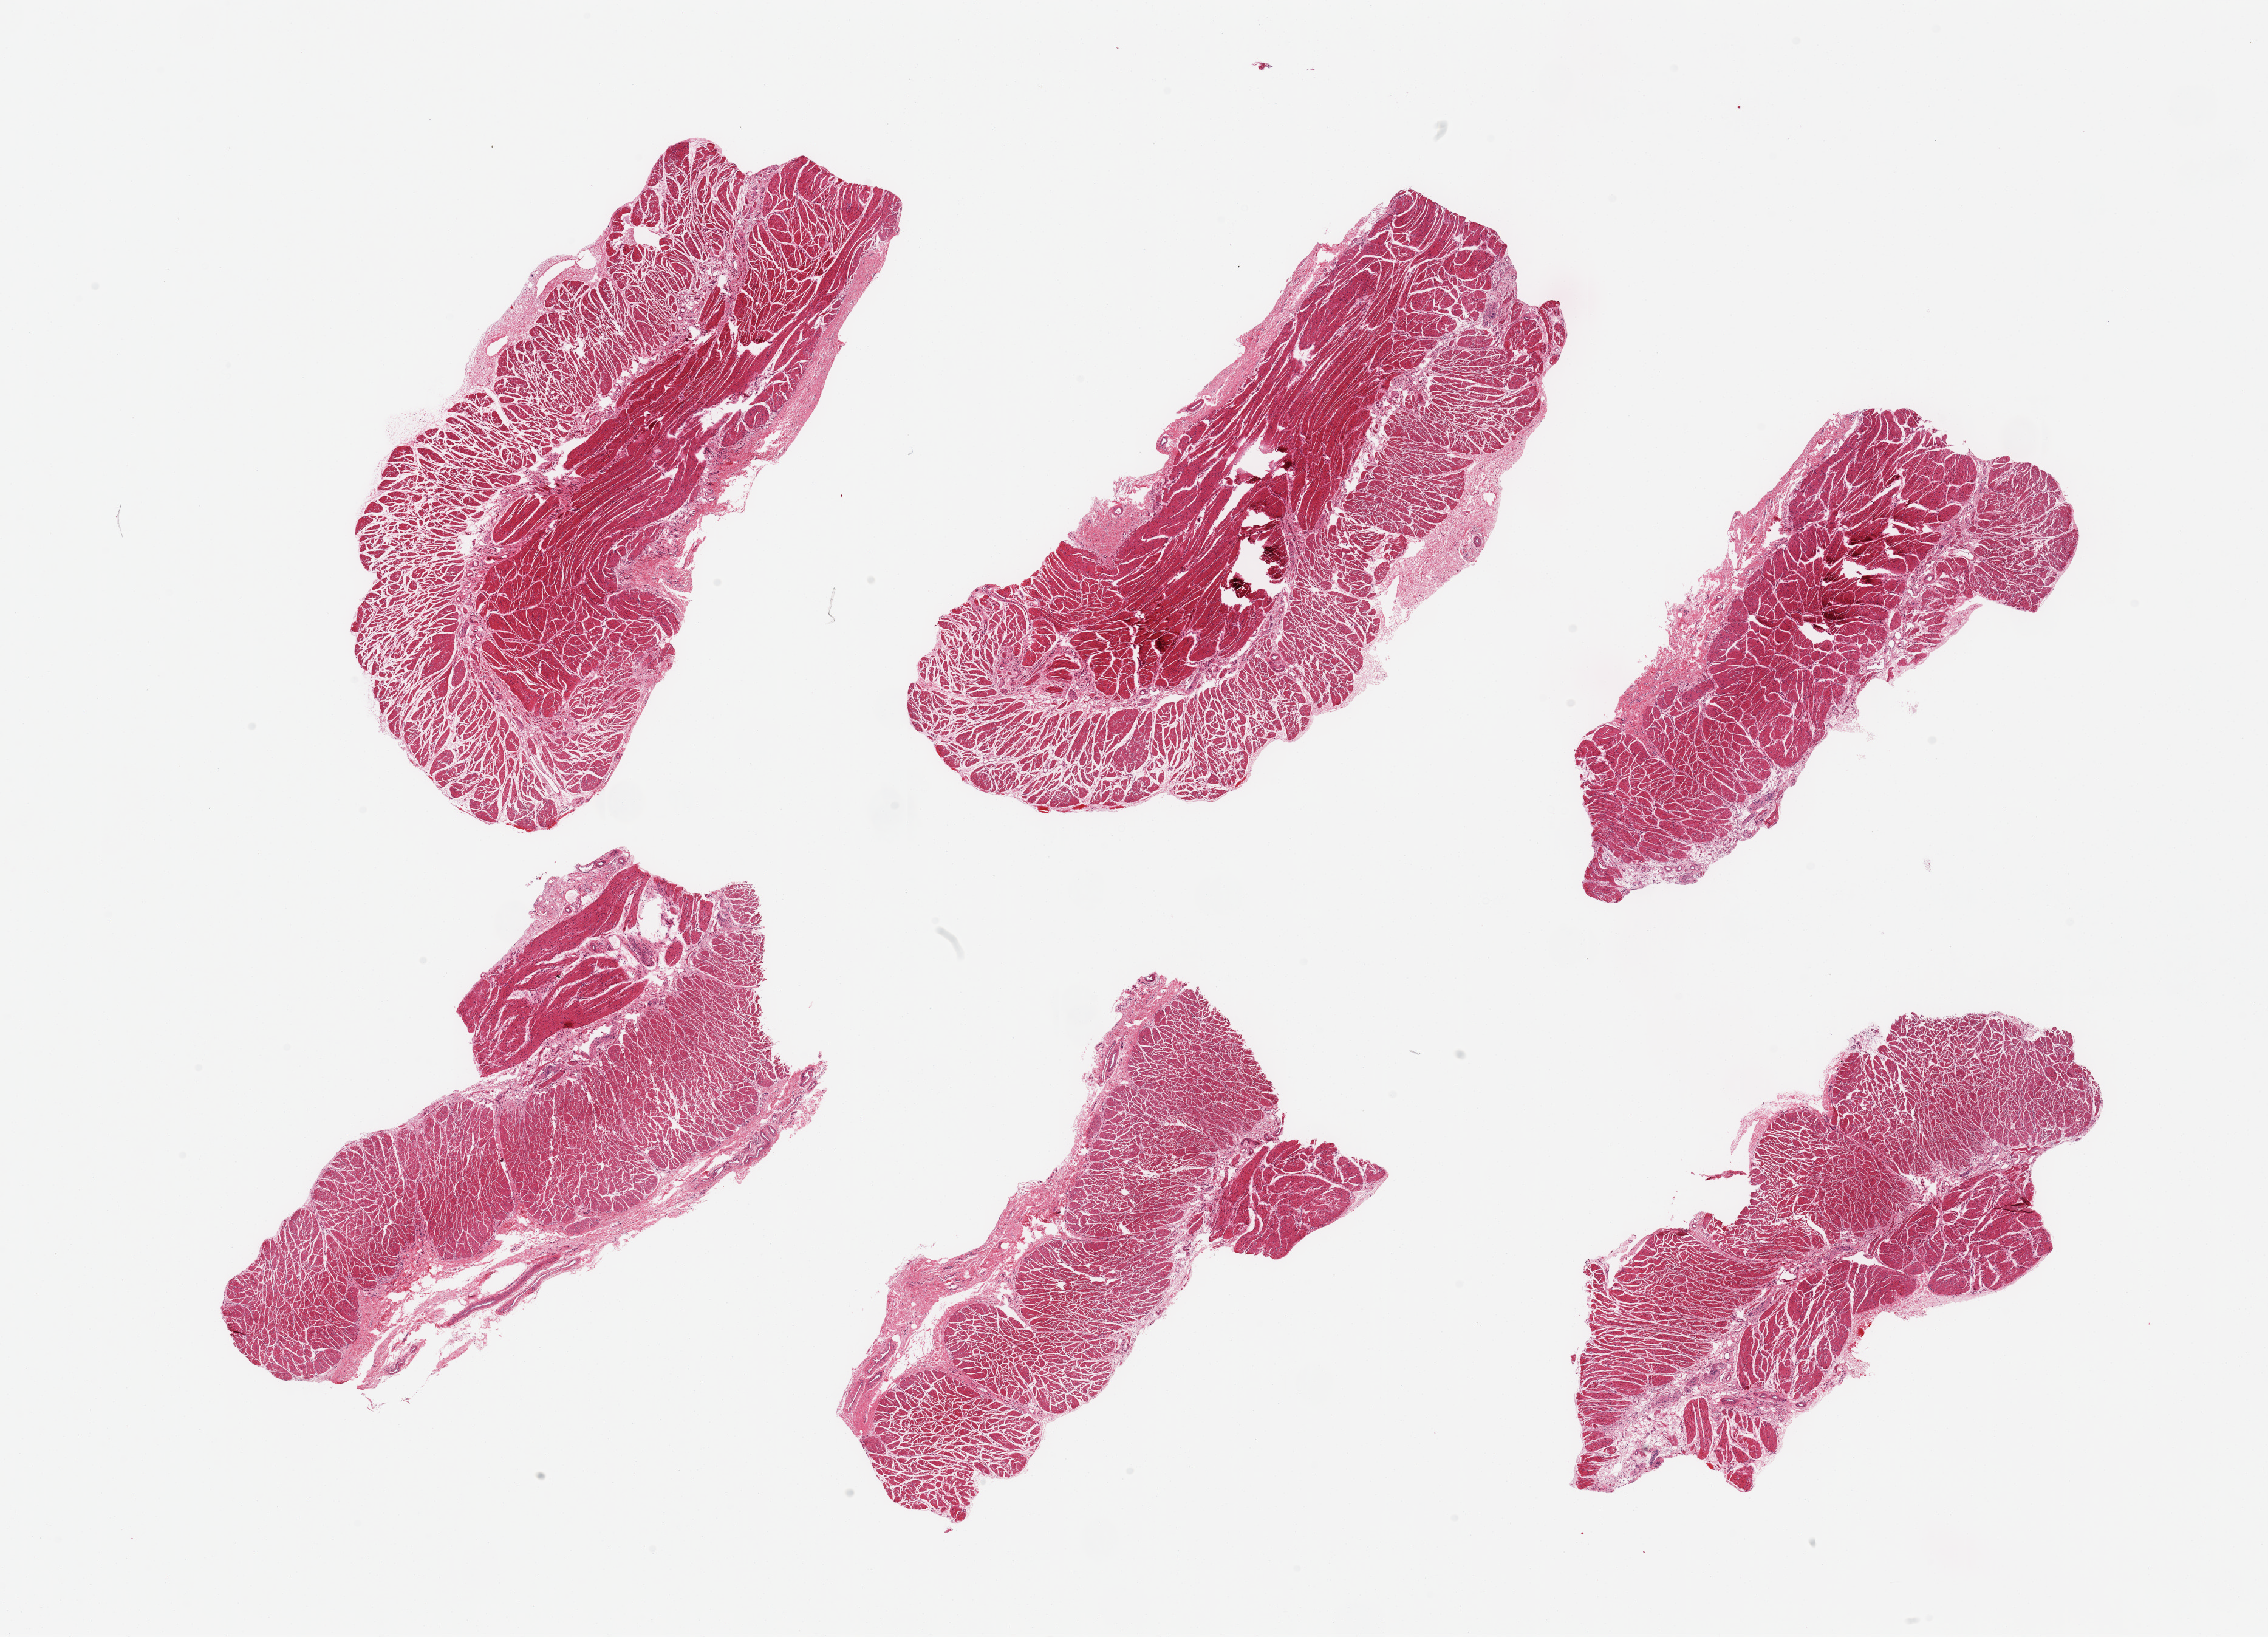
Digitized haematoxylin and eosin-stained section, a low-resolution overview of the entire scanned area, about 29.5 x 21.3 mm, PAXgene-fixed, paraffin-embedded tissue, target tissue: esophageal muscle, donor tissue sample. Donor: female.
Pathologist's review note for this sample: 6 pieces; well trimmed muscularis.